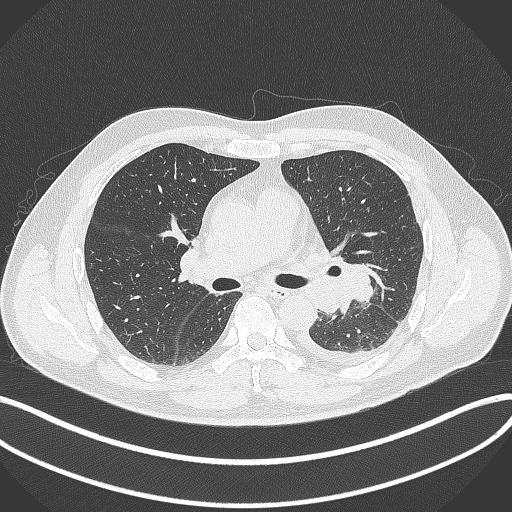
Chest CT, one axial slice. Position 213 of 342 along the scan axis. Reconstruction kernel B70f. 120 kVp. Lung window (W 1500 / L -600 HU). 512 × 512 image matrix. Male patient, age 58 years. Case-level facts recorded for this patient, not image findings: clinical TNM (as recorded): T3 N1 M1b.
Outlined on this slice (rectangle marked by the reading radiologist):
- lung tumour (recorded histology: small cell carcinoma): bounding box (x1, y1, x2, y2) in pixels: (342, 255, 383, 306)